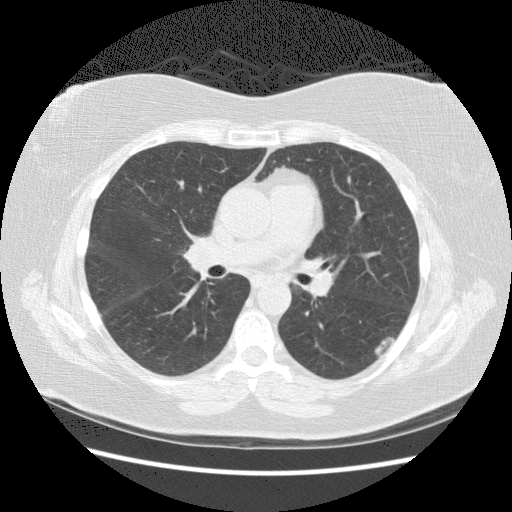
Axial slice from a low-dose chest CT screening exam. Second screening round (one year after baseline). Lung window (W 1500 / L -600 HU). 2.5 mm slice thickness. Slice 78 of 140 in the series. 512 × 512 image matrix. Female, age 57 years at enrolment.
Lesion marked by an expert reader, bounding box (x1, y1, x2, y2) in pixels: (363, 329, 402, 367). Reader record for this screening exam (exam-level; its link to the box is not recorded): non-calcified nodule or mass ≥4 mm, left lower lobe, 19 × 9 mm, poorly defined margins, mixed attenuation, pre-existing on the prior screen: yes; interval growth: yes. Participant outcome: lung cancer diagnosed 560 days after this screen — squamous cell carcinoma, NOS, left lower lobe, poorly differentiated (G3), stage IB (AJCC 6th edition), 40 mm at pathology.